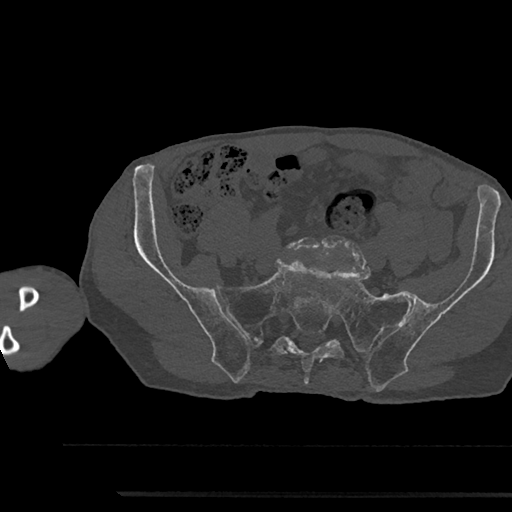
CT including the spine, one axial slice; position 283 of 797 along the scan axis; reconstruction kernel Br40s/3; 120 kVp; bone window (W 1800 / L 400 HU); 0.5 mm slice thickness; 512 × 512 image matrix. Patient: male, 79 years. Case-level facts recorded for this patient, not image findings: primary cancer: prostate.
Annotated regions visible in this slice (semi-automatic segmentation, software-assisted and operator-edited):
- L5 vertebra: bounding box <287,237,351,252> (left, top, right, bottom; pixels)